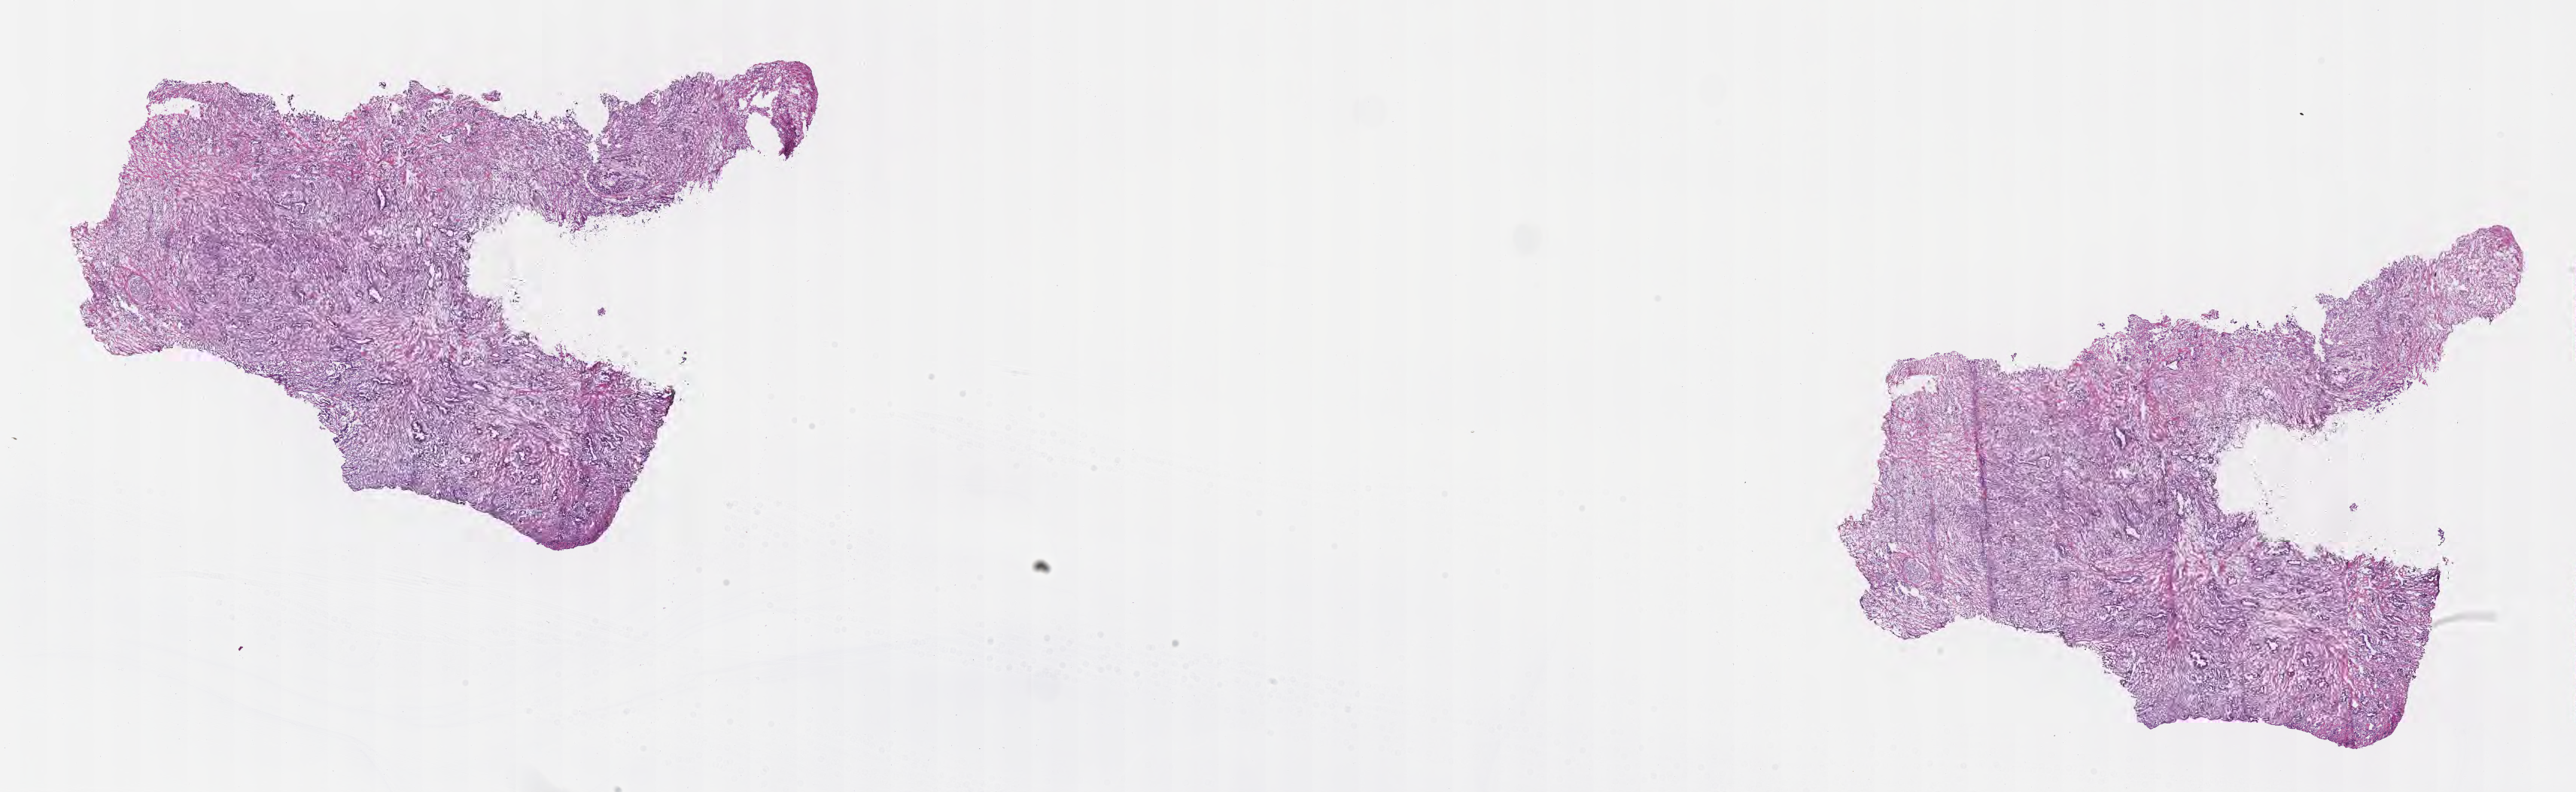
Digitized hematoxylin and eosin (H&E)-stained section, a low-resolution overview of the entire scanned area, about 27.7 x 8.5 mm, frozen section (tissue freezing medium), specimen: primary tumor, anatomic site: head of pancreas. Patient: female, age at initial diagnosis 75 years. Slide review estimates, as recorded: tumor cells 38%, tumor nuclei 72%, stromal cells 57%, necrosis 5%, normal cells 0%. Inflammatory infiltration, as recorded: lymphocyte infiltration 14%, monocyte infiltration 3%, neutrophil infiltration 0%.
- section: bottom of the tissue portion
- diagnosis: Infiltrating duct carcinoma, NOS